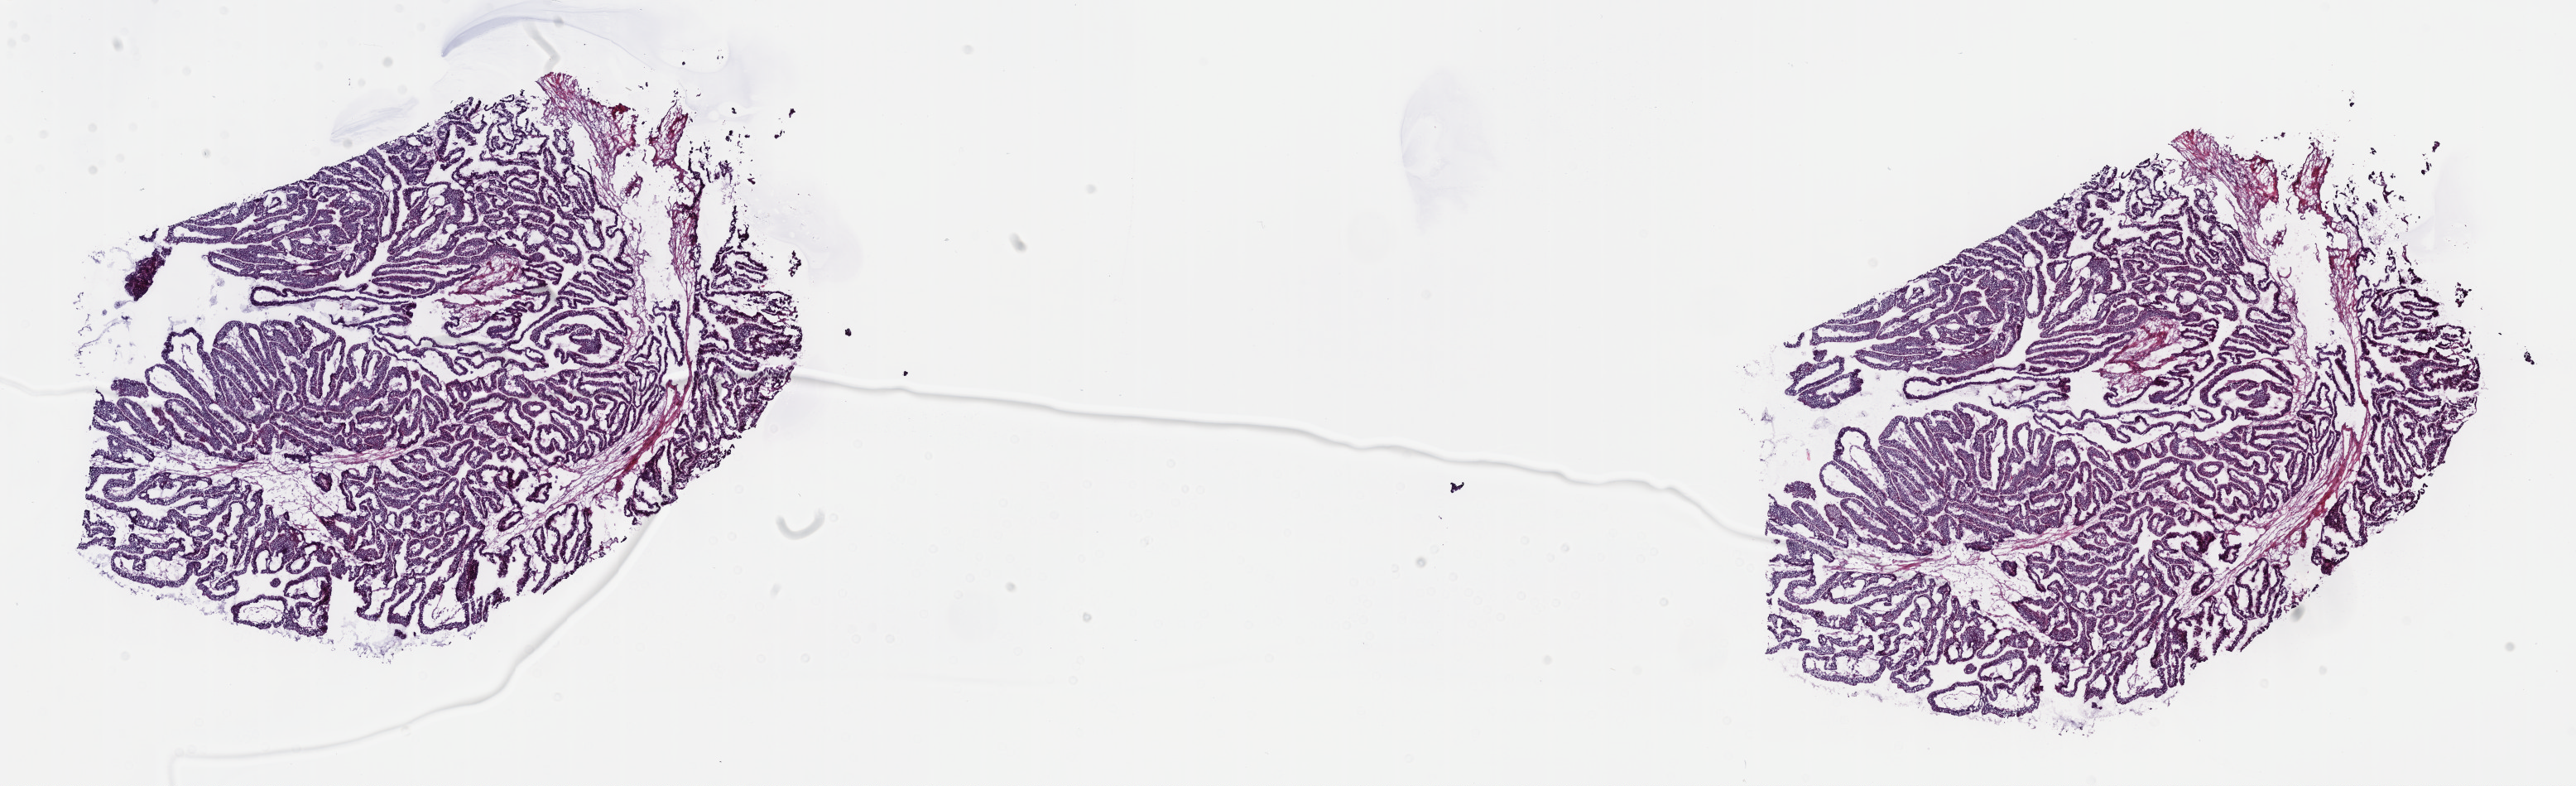
Digitized Hematoxylin and eosin (H&E) stained tissue section (whole slide), low-resolution overview of the scanned area, about 25.2 x 7.7 mm. Frozen section from the top of the tissue portion. Pancreas, primary tumour sample. Male, age 71 years at initial diagnosis.
Histologic diagnosis: Infiltrating duct carcinoma, NOS.